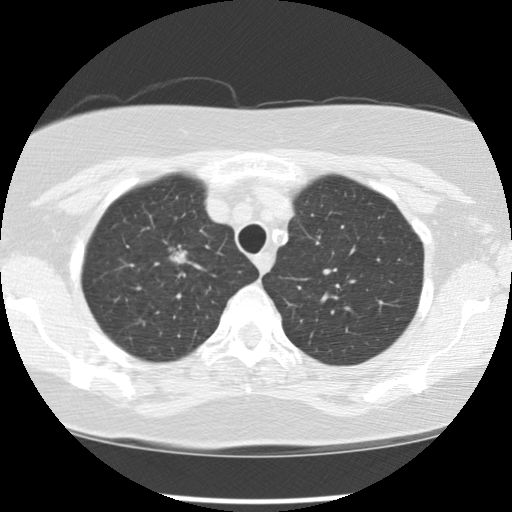
Low-dose screening chest CT, one axial slice; reconstruction kernel STANDARD; 120 kVp; lung window (W 1500 / L -600 HU); 2.5 mm slice thickness; 512 × 512 image matrix, field of view 318 × 318 mm.
Annotated regions visible in this slice (expert manual segmentation):
- lesion 1 (tumor, upper lobe of right lung): bounding box (x1, y1, x2, y2) in pixels: (169, 245, 187, 264)